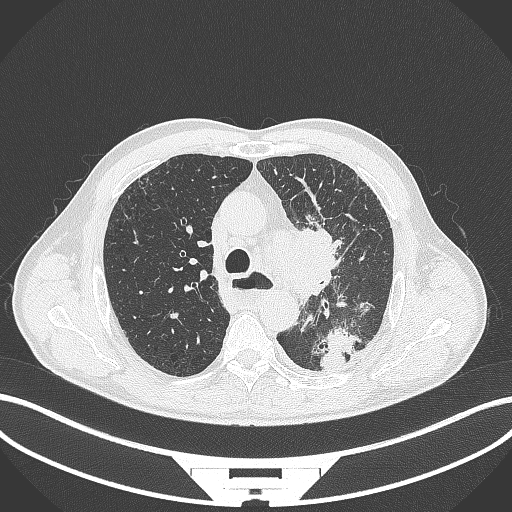
Chest CT, one axial slice. Slice 268 of 411 in the series (ordered by position). Reconstruction kernel B70f. 120 kVp. Lung window (W 1500 / L -600 HU). 1 mm slice thickness. 512 × 512 image matrix, field of view 400 × 400 mm. Male patient, age 57 years. Case-level facts recorded for this patient, not image findings: clinical TNM (as recorded): T2a N1 M0.
Outlined on this slice (bounding box drawn by a radiologist):
- lung tumour (recorded histology: squamous cell carcinoma): bounding box <294,224,343,302> (left, top, right, bottom; pixels)